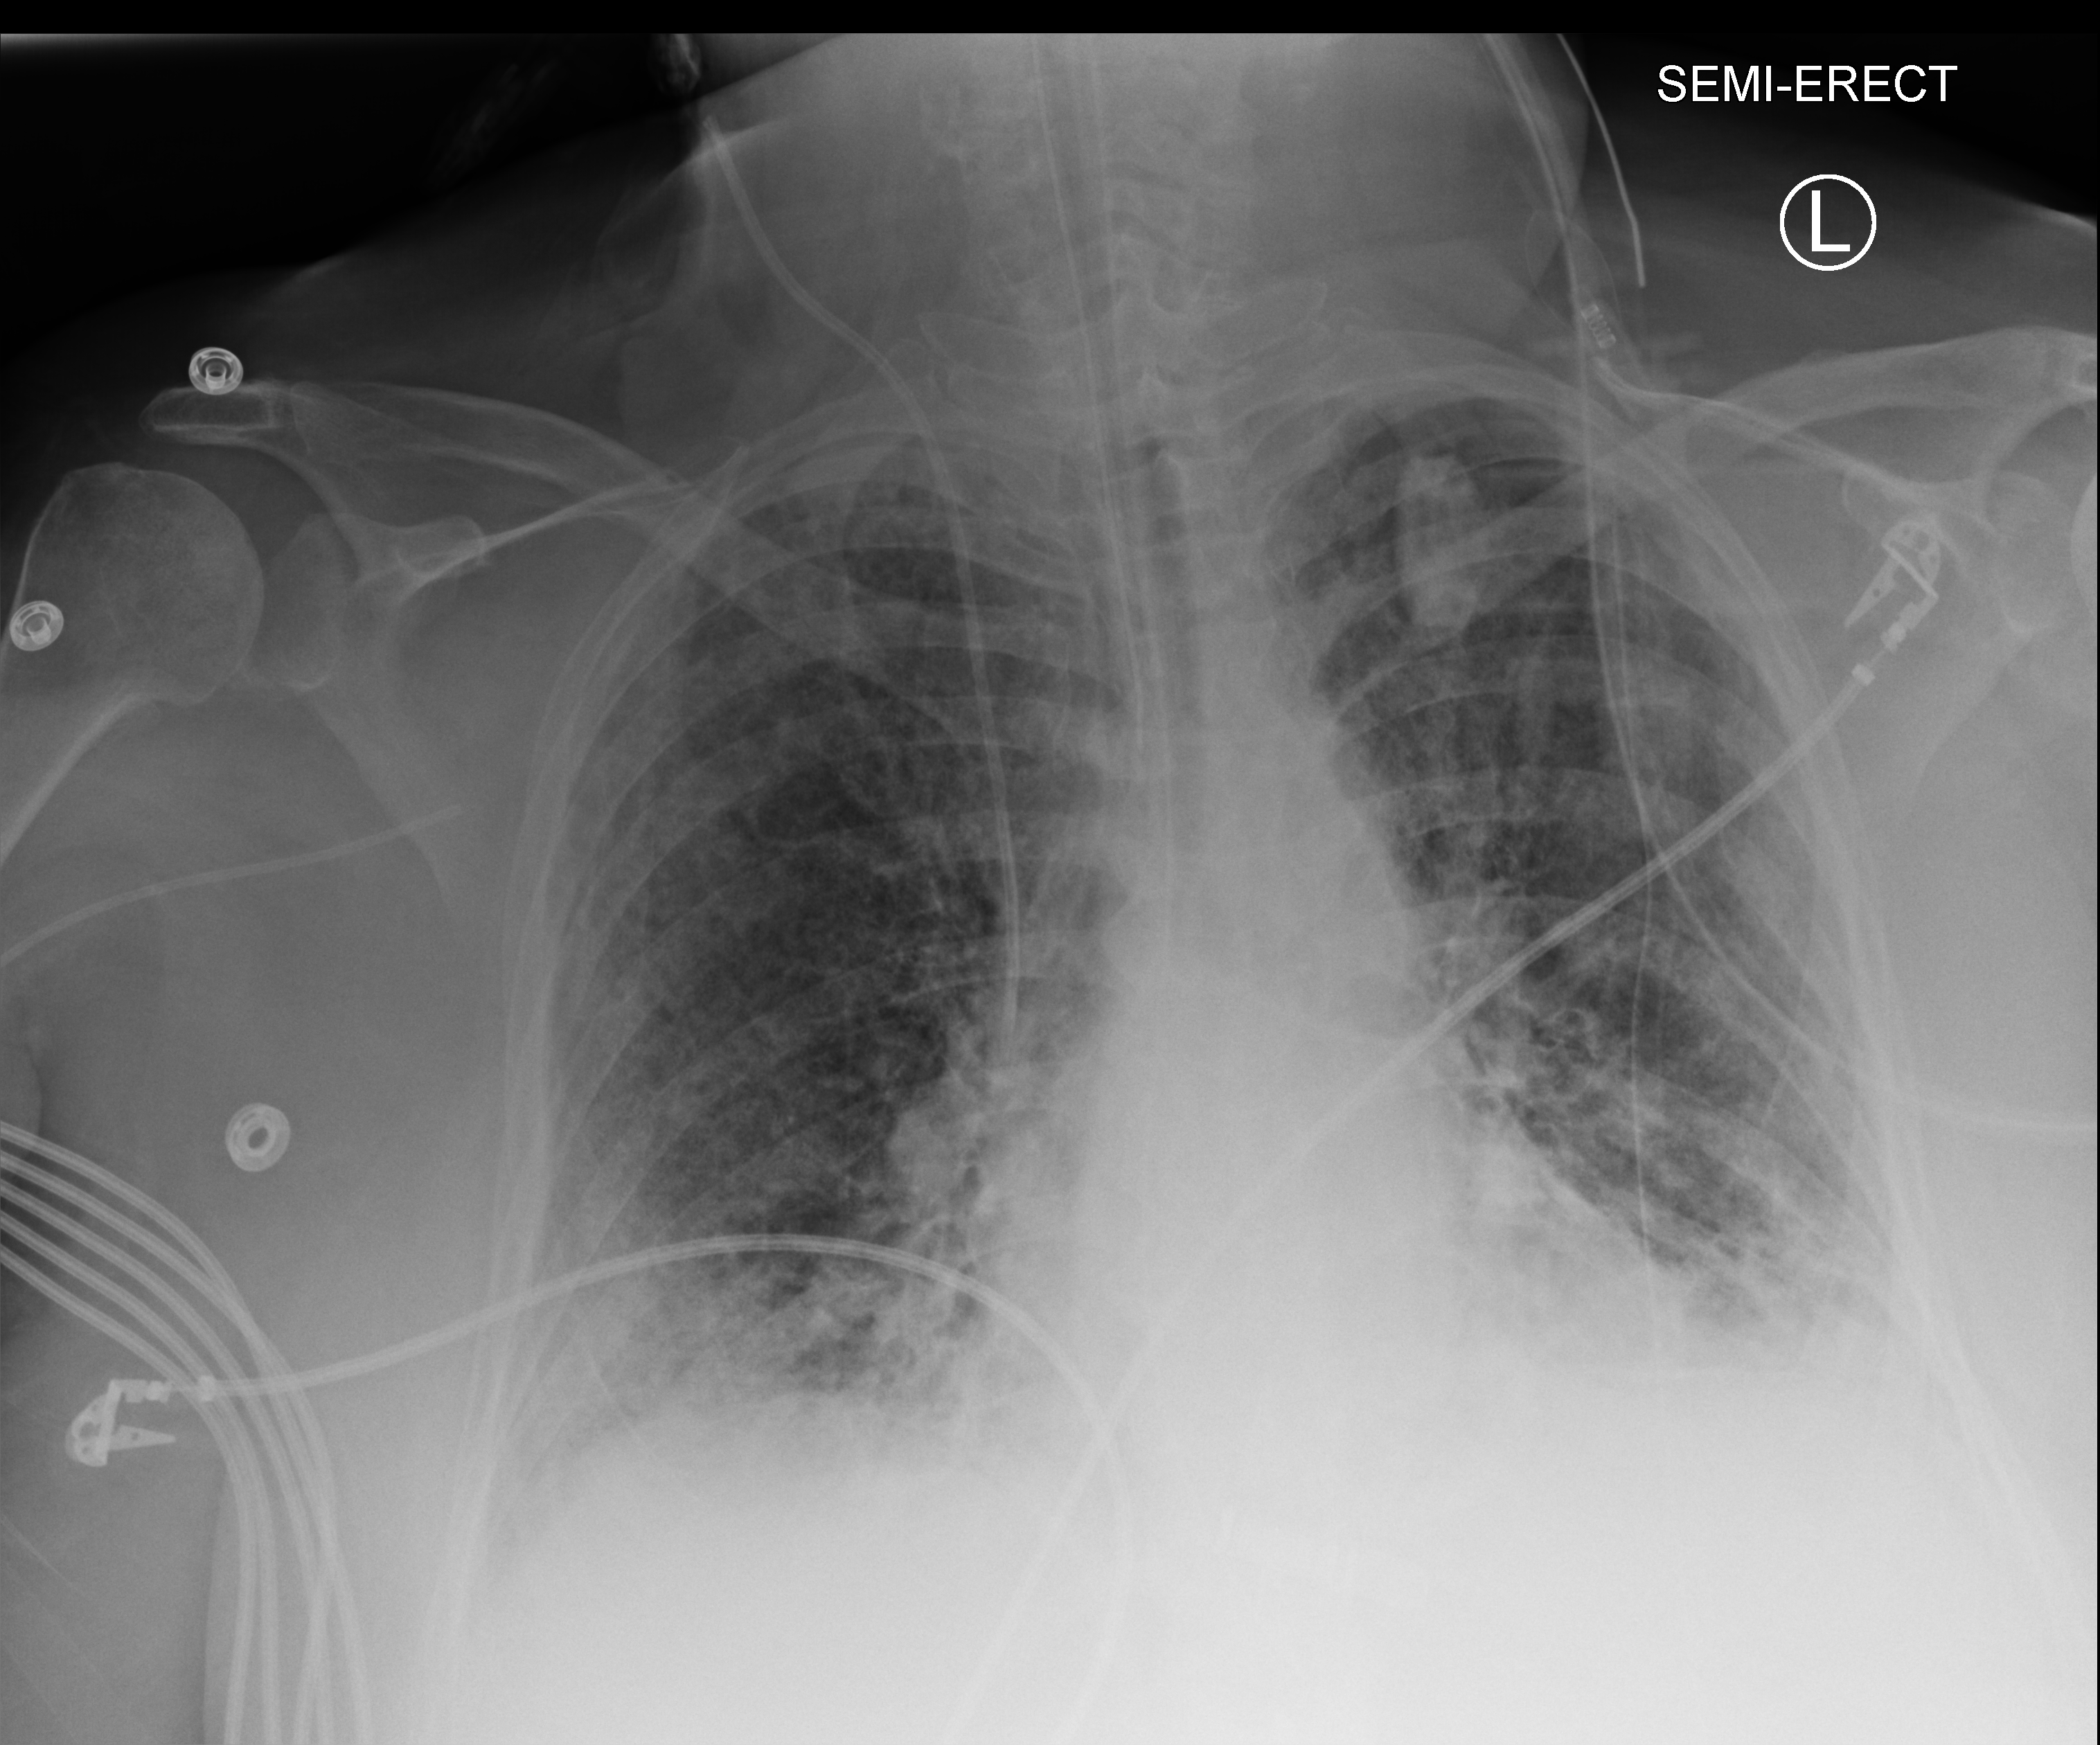
Portable chest radiograph; anteroposterior (AP) projection. Patient hospitalised with COVID-19; female, aged 60–74 years.
Admission-level facts for this patient (not findings on this image; timing relative to this image not recorded):
- admitted to intensive care during this hospital stay: yes